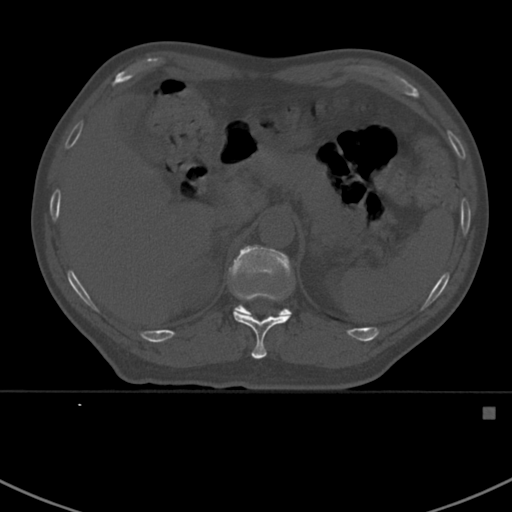
CT including the spine, one axial slice; position 342 of 412 along the scan axis; bone window (W 1800 / L 400 HU); 512 × 512 image matrix, field of view 358 × 358 mm. Male patient, age 59 years. From the clinical record (not read from this slice): primary cancer: prostate.
Outlined on this slice (semi-automatically segmented with operator editing):
- T11 vertebra: box from (x=234, y=294) to (x=292, y=359) px
- T12 vertebra: (x=229, y=246)–(x=292, y=315)